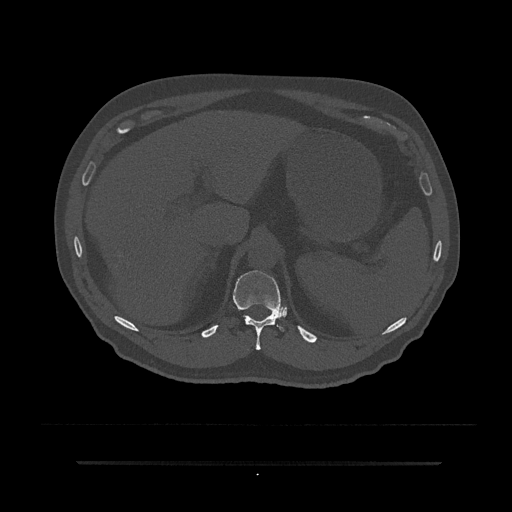
CT including the spine, one axial slice. Bone window (W 1800 / L 400 HU). 0.5 mm slice thickness. 512 × 512 image matrix, field of view 464 × 464 mm. Male patient, age 59 years. Case-level facts recorded for this patient, not image findings: primary cancer: bile ducts; vertebrae with lytic lesions (as recorded): T10.
Structures marked on this image (semi-automatic segmentation, software-assisted and operator-edited):
- T11 vertebra: bounding box <233,271,284,350> (left, top, right, bottom; pixels)